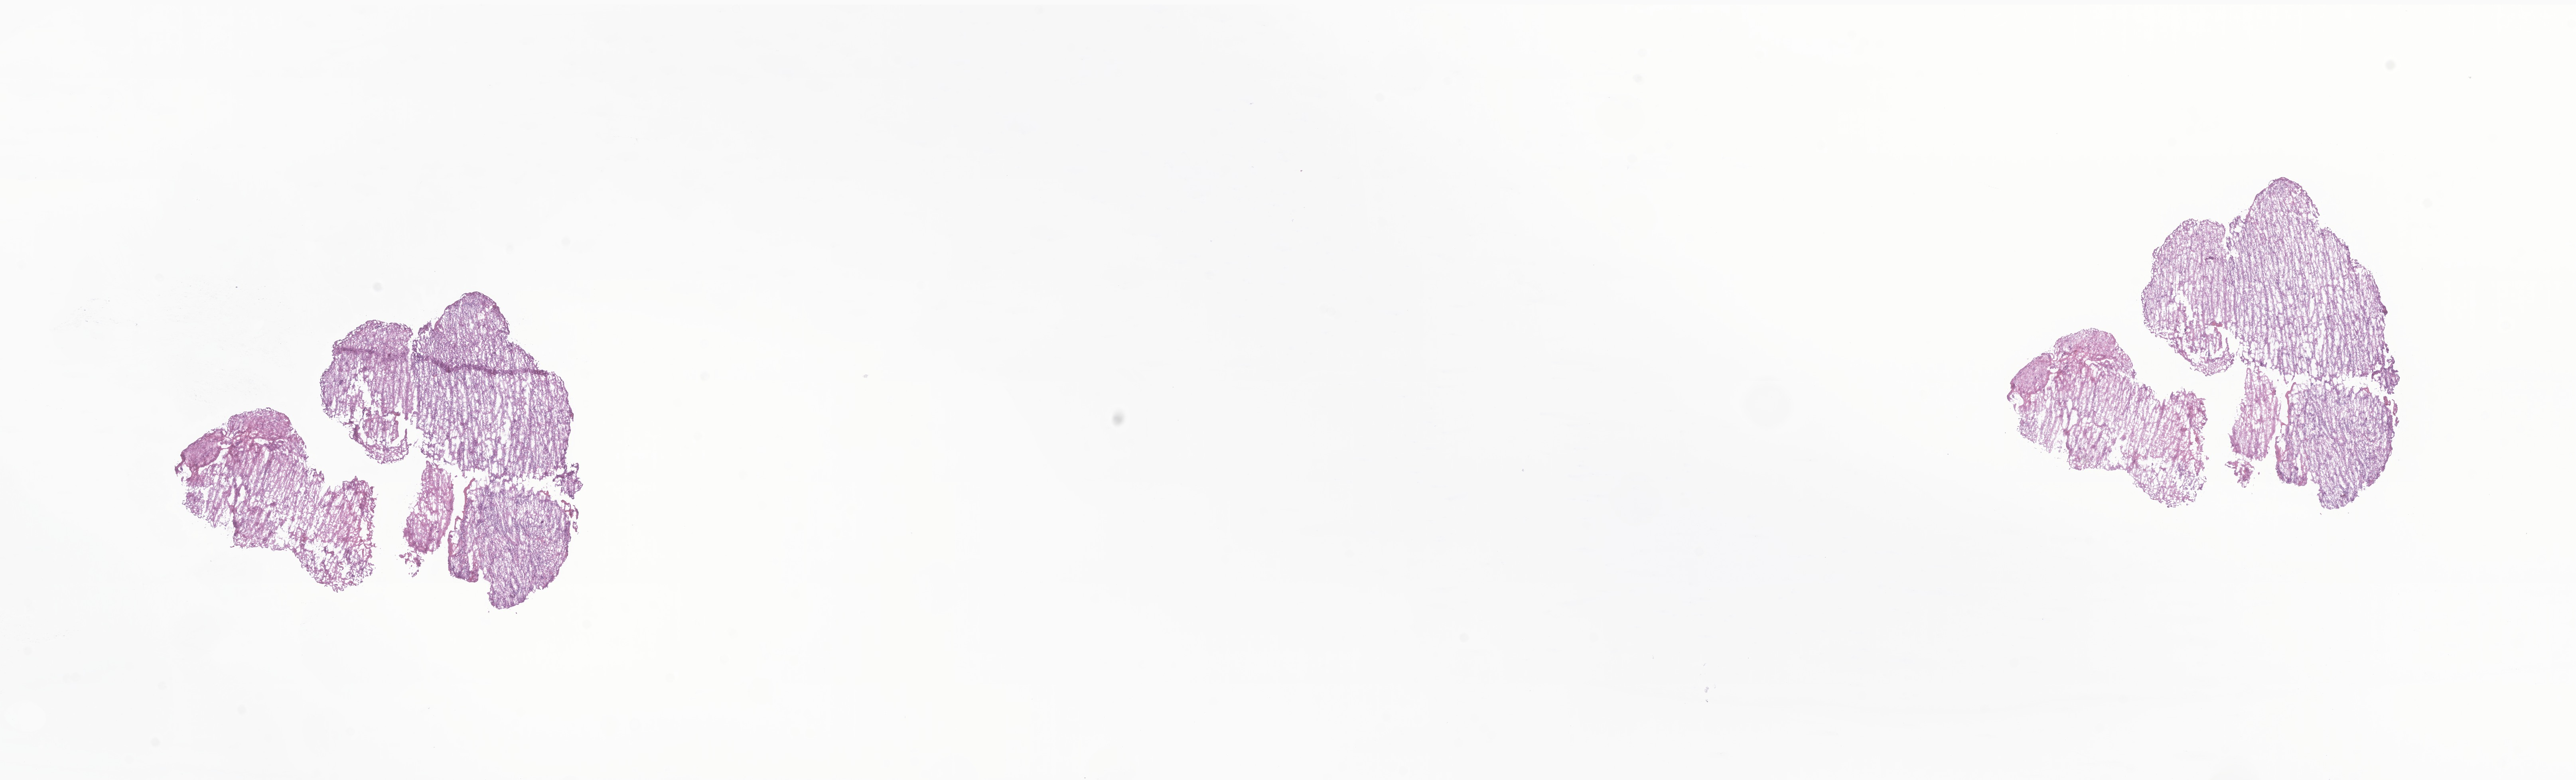
Whole-slide image, H&E stain of tumor tissue from the brain — whole scanned area (about 27.2 x 8.2 mm) shown as a low-resolution overview; frozen section. Male patient, age 188 months (15 years 8 months).
Recorded diagnosis: Neoplasm, uncertain whether benign or malignant.